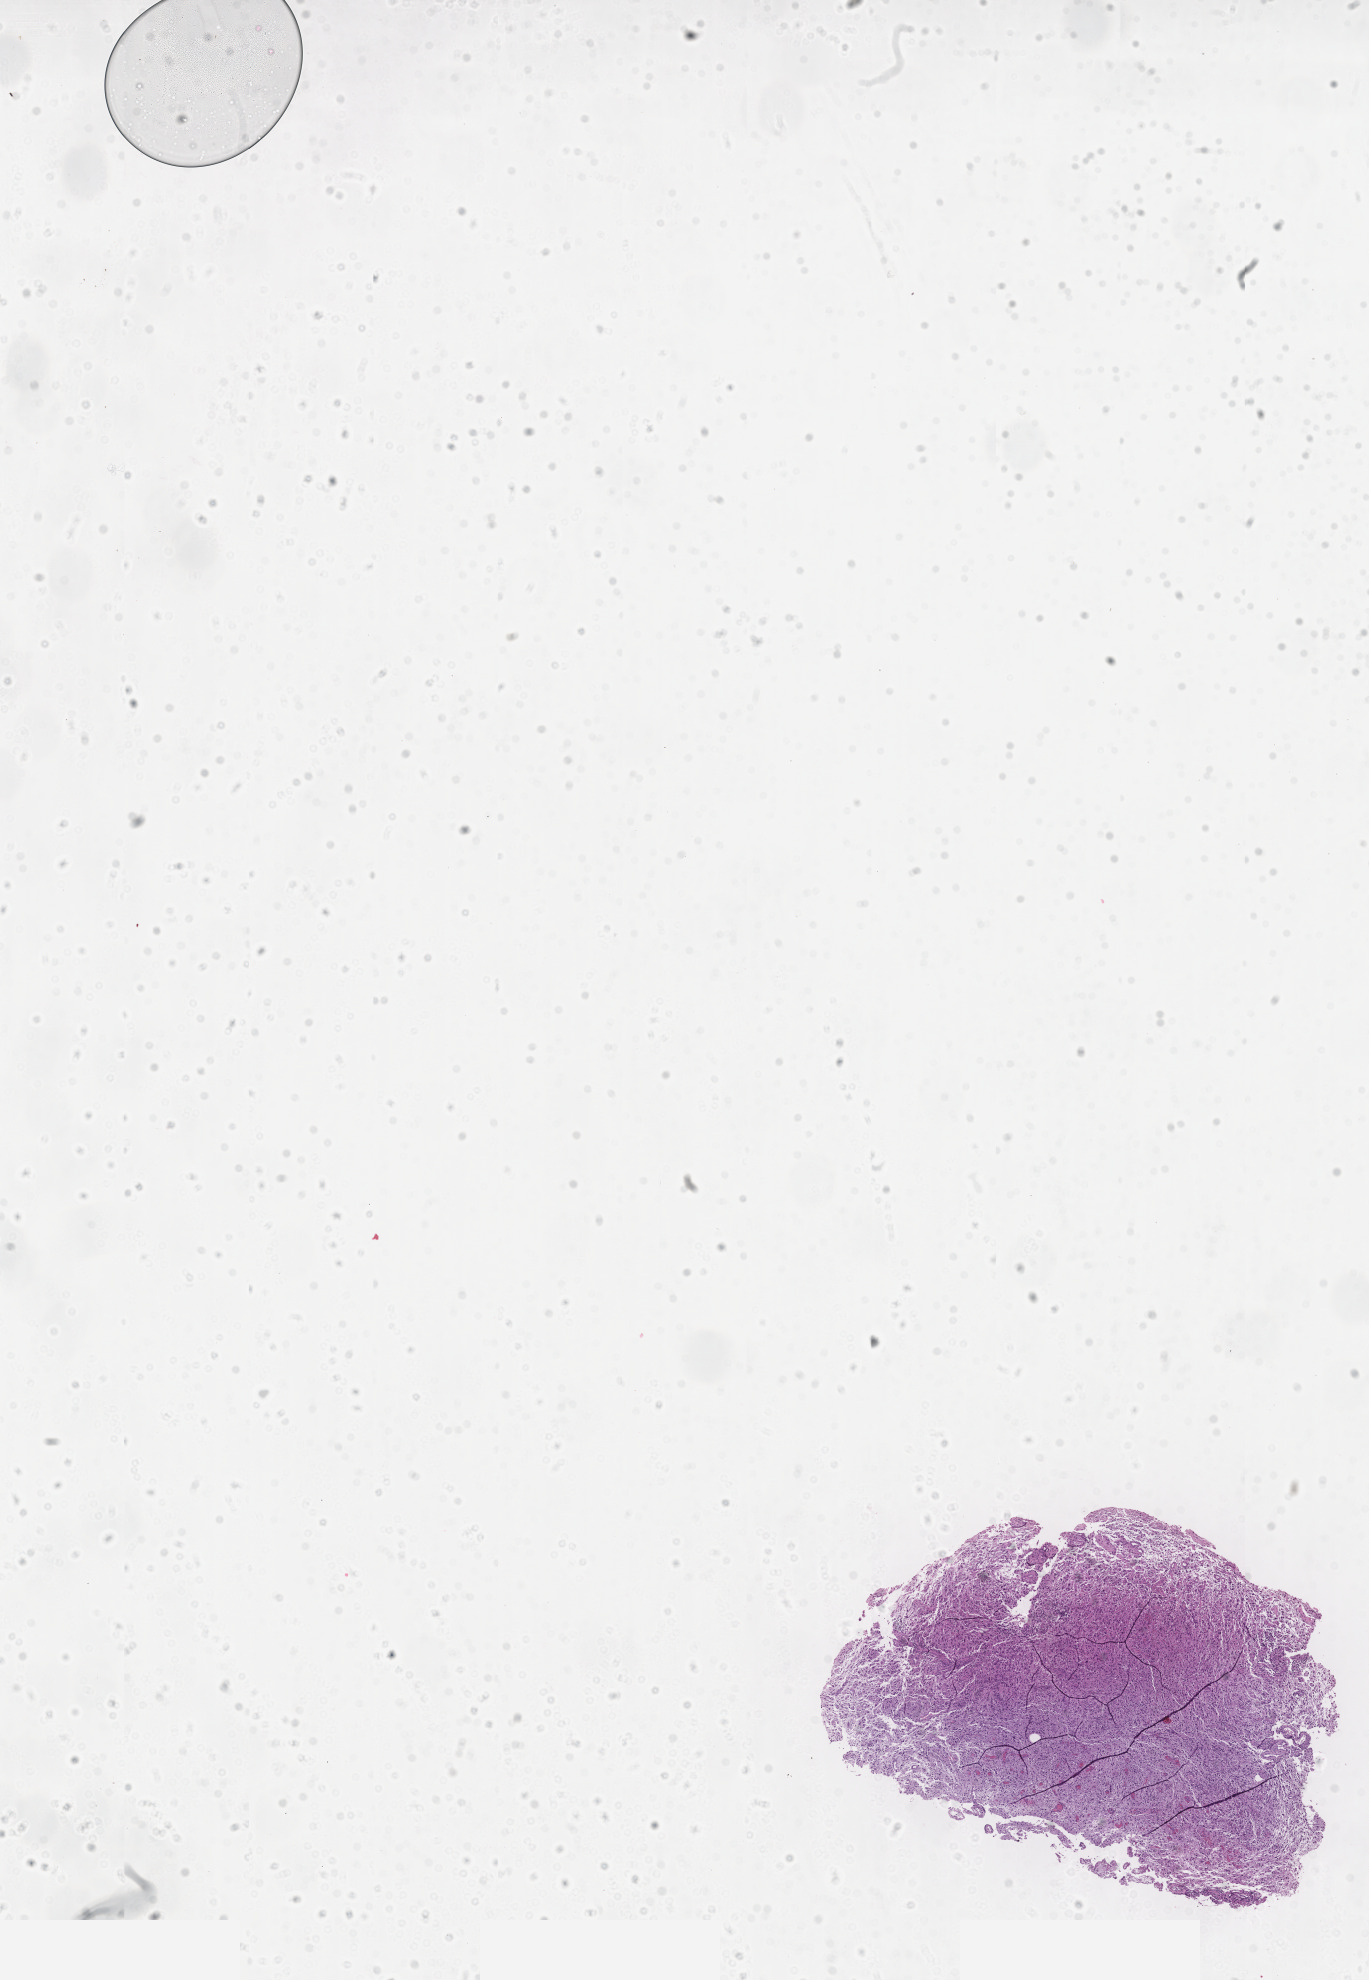
H&E whole-slide image, low-resolution overview of the scanned area, about 11.0 x 16.0 mm (slide scanned at 20x); tumour tissue sample, sampled site: brain. 48-year-old female patient. Pathologist review of this section (percent, as recorded): tumour nuclei 80%, necrosis 3%.
Primary tumour site (as recorded): temporal lobe. Histologic diagnosis: Glioblastoma.